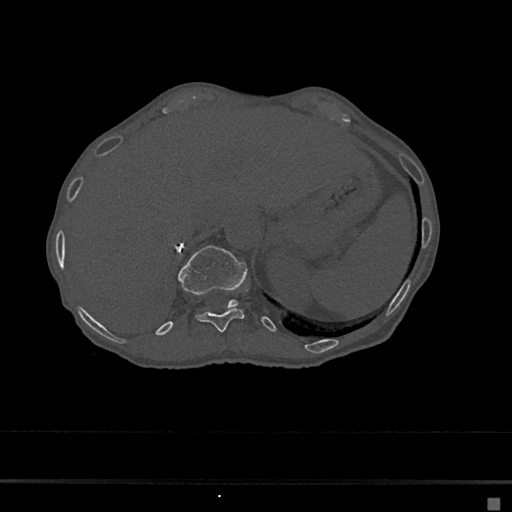
CT including the spine, one axial slice; 120 kVp; bone window (W 1800 / L 400 HU); 0.5 mm slice thickness; 512 × 512 image matrix. Patient: female, 68 years. From the clinical record (not read from this slice): primary cancer: renal.
Annotated regions visible in this slice (semi-automatically segmented with operator editing):
- T10 vertebra: box from (x=223, y=347) to (x=225, y=350) px
- T11 vertebra: (x=196, y=289)–(x=248, y=332)
- T12 vertebra: (x=178, y=245)–(x=247, y=308)